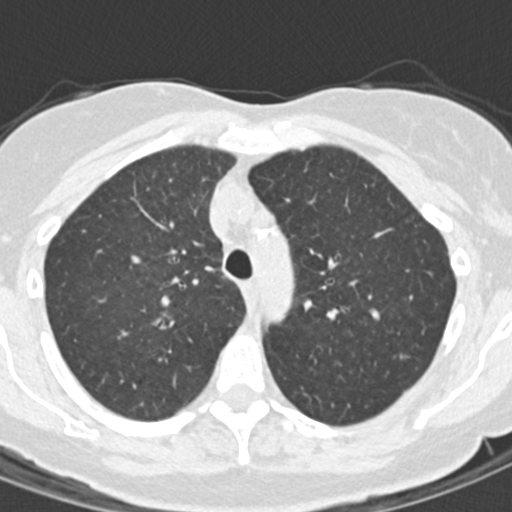
Low-dose screening chest CT, one axial slice. Reconstruction kernel B30f. 120 kVp. Lung window (W 1500 / L -600 HU). 512 × 512 image matrix, field of view 280 × 280 mm.
Outlined on this slice (outlined manually by an expert reader):
- lesion 1 (tumor, upper lobe of right lung): box from (x=151, y=312) to (x=175, y=330) px